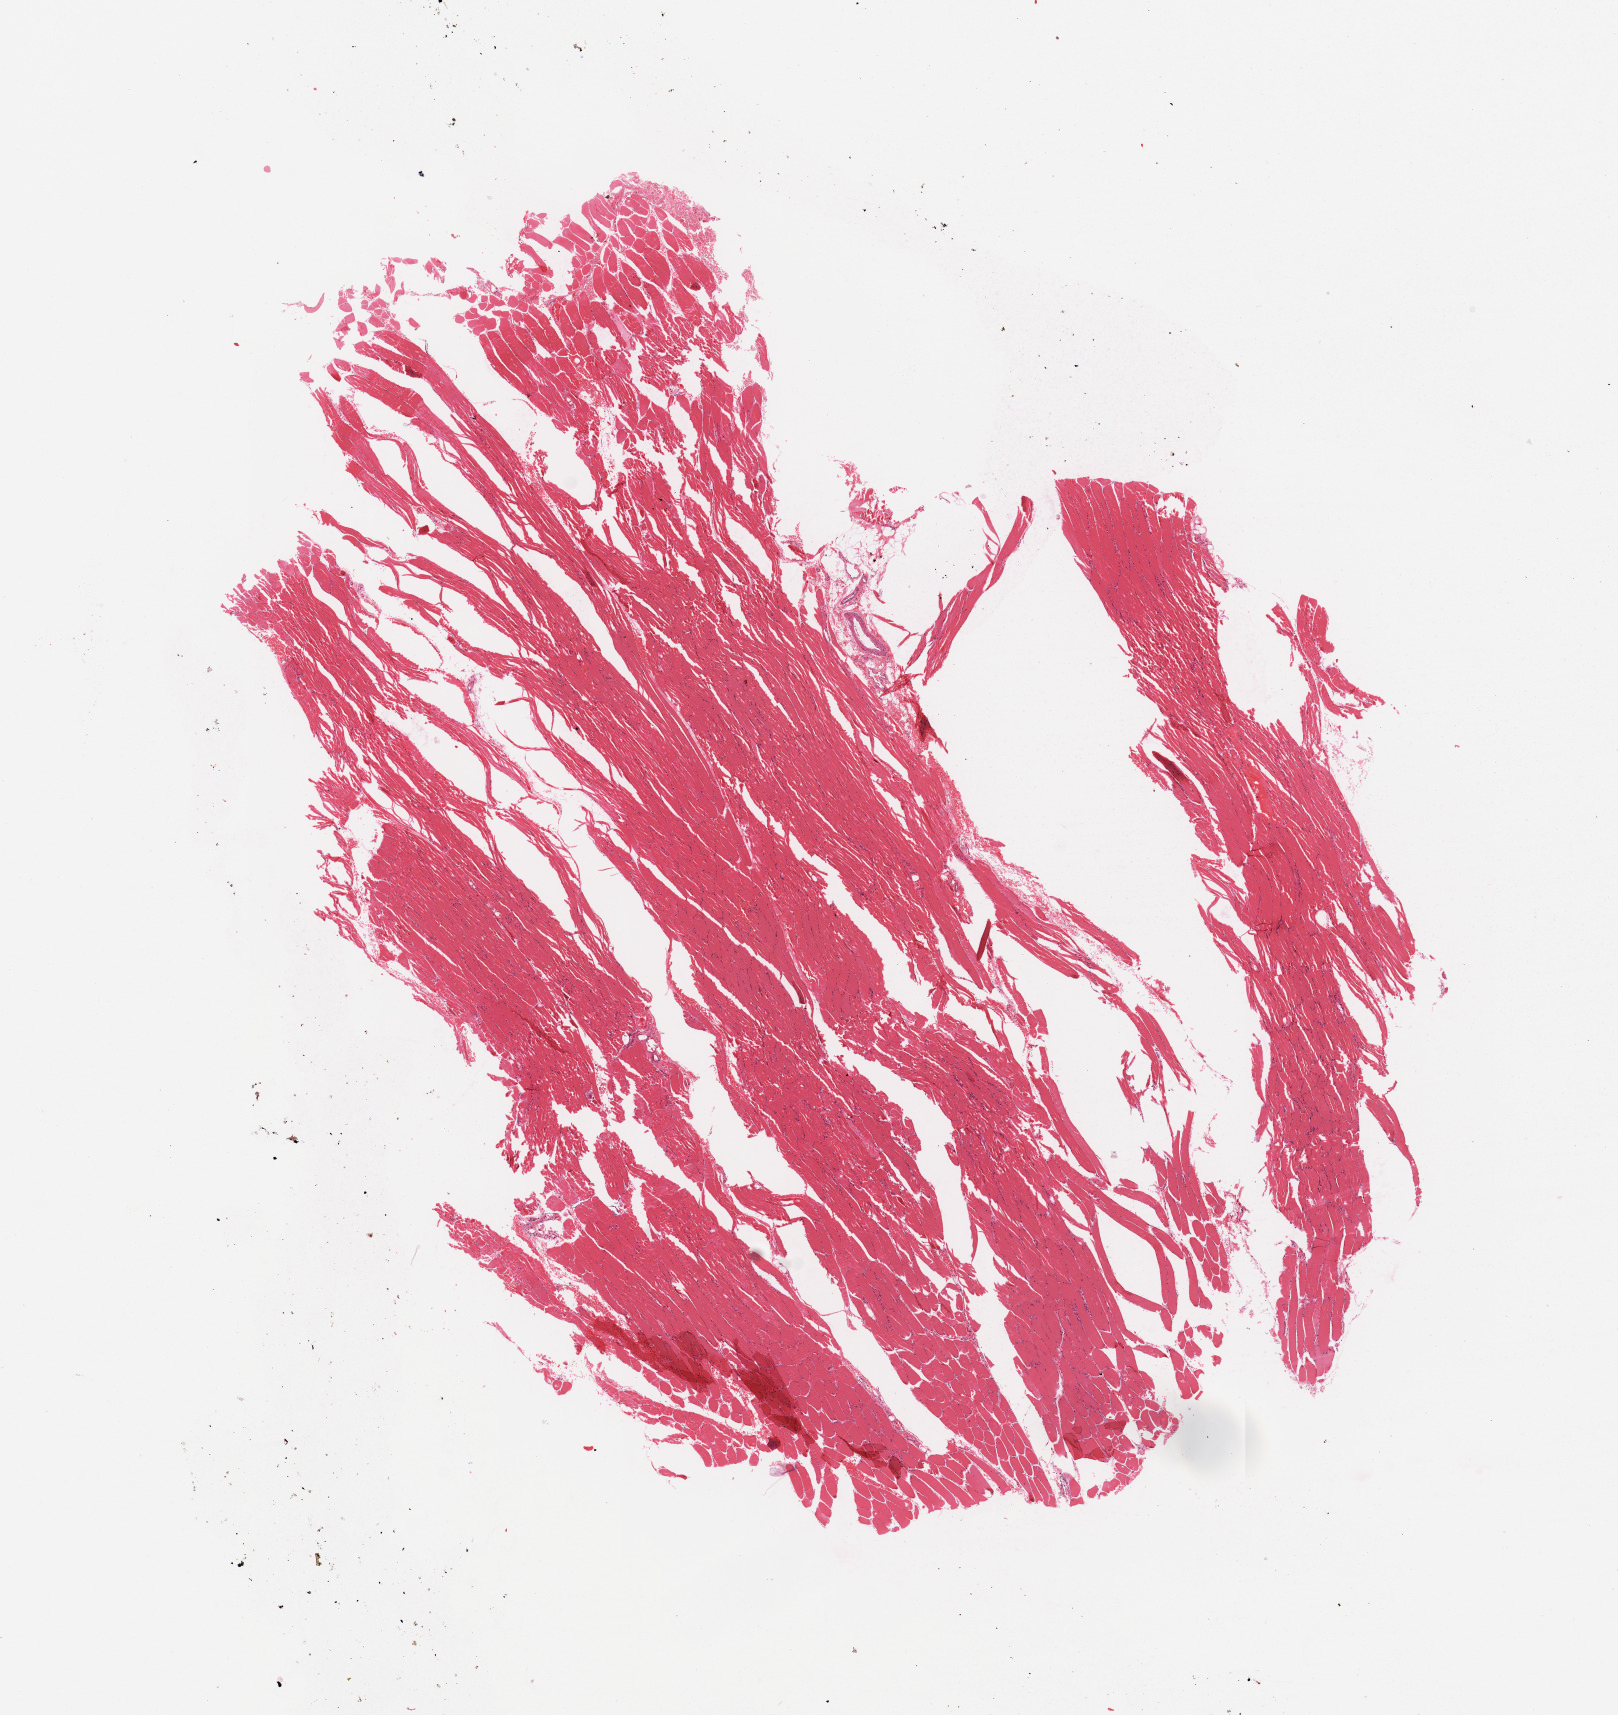
Whole-slide histology image, H&E-stained, a low-resolution overview of the entire scanned area, about 12.8 x 13.6 mm. Normal (non-tumour) tissue sample. 54-year-old male patient.
This section: normal (non-tumour) tissue from the same patient. Patient diagnosis (cohort enrolment): sarcoma (site not recorded at cohort level).